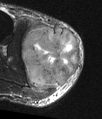
MRI of an extremity soft-tissue mass, one axial slice; position 27 of 48 along the scan axis; T2-weighted fat-saturated; MR volume resampled by the dataset authors to the PET/CT grid (not the native acquisition matrix); 3.27 mm slice thickness; 102 × 119 image matrix, field of view 100 × 116 mm. Male patient. From the clinical record (not read from this slice): histological type: pleiomorphic liposarcoma; grade: high; site of the primary tumour: right calf.
Annotated regions visible in this slice (expert contour drawn on MRI and transferred to this co-registered scan by the dataset authors):
- gross tumour volume including surrounding oedema: bounding box [x1, y1, x2, y2] px = [21, 26, 79, 91]
- gross tumour volume (mass): [21, 28, 79, 88]